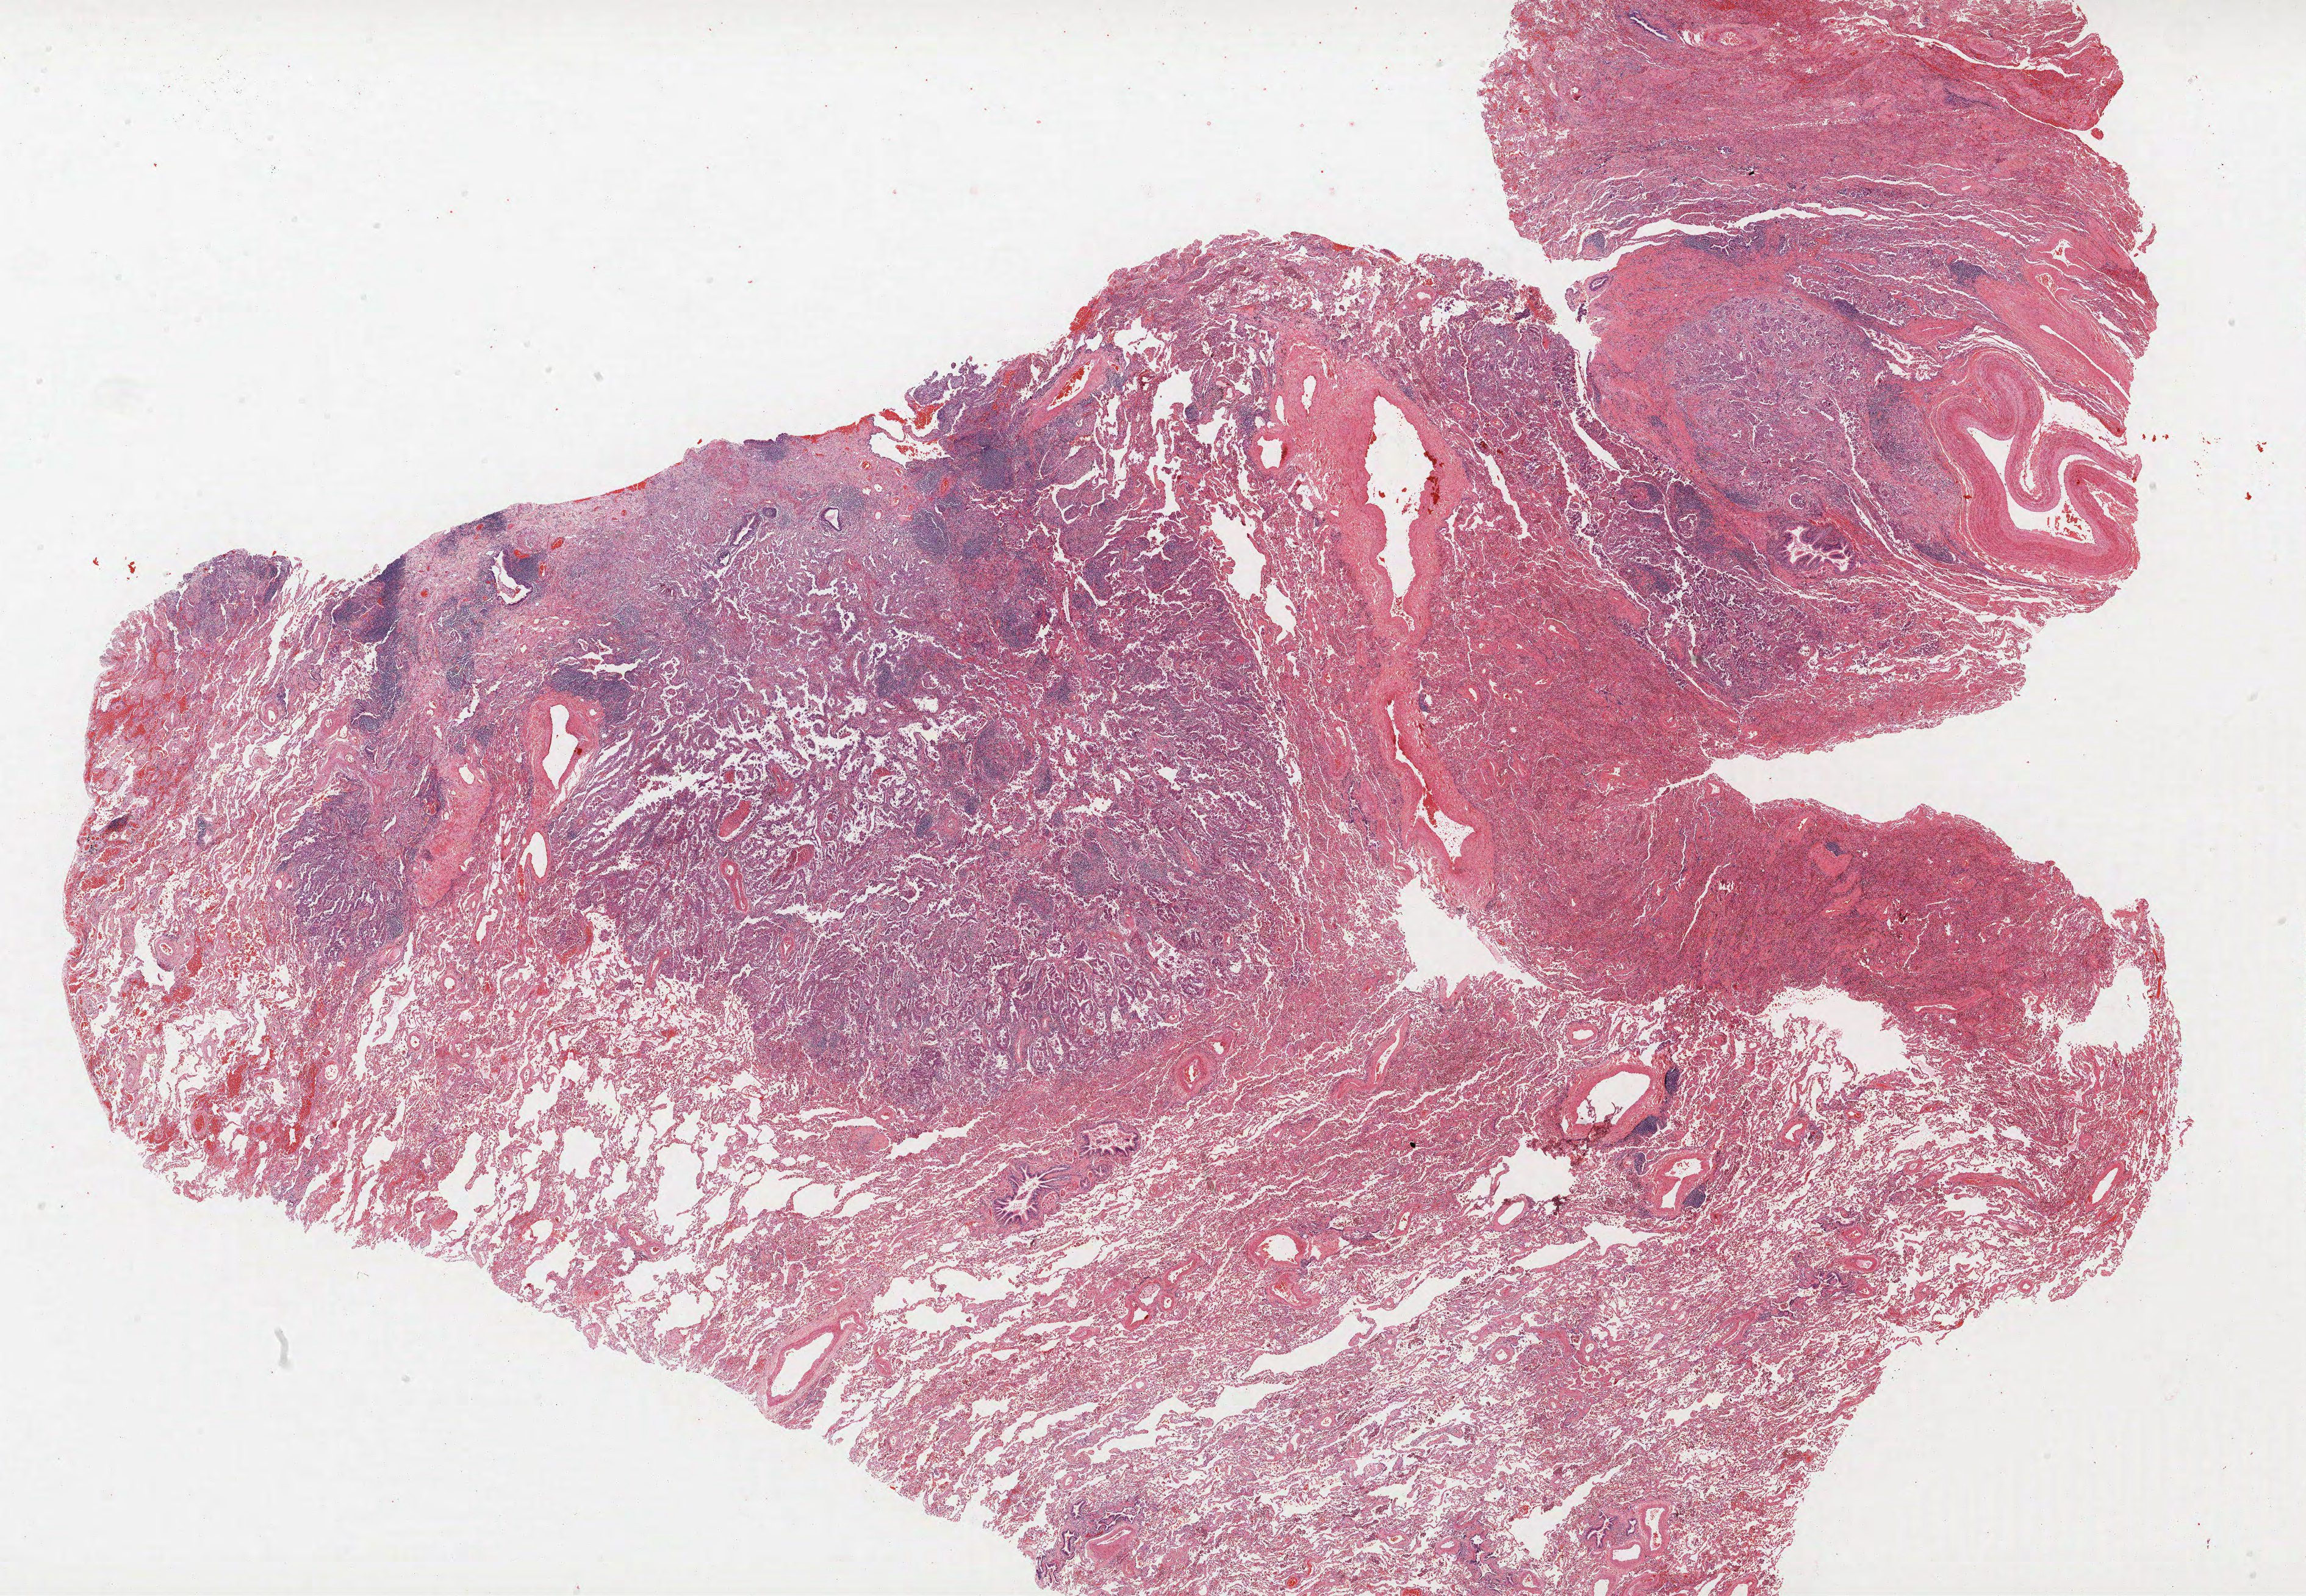
Whole-slide histology image, H&E, whole scanned area (about 30.2 x 20.9 mm, slide scanned at 40x) shown as a low-resolution overview; formalin-fixed paraffin-embedded (FFPE) section; lung tissue. Male patient, aged 71 at enrolment. Current smoker at enrolment. Grade: moderately differentiated (G2).
Participant's lung-cancer diagnosis: Adenocarcinoma, NOS. Stage (AJCC 6th edition): IA. Tumour size (pathology): 24 mm. Primary tumour location (clinical record): right lower lobe.